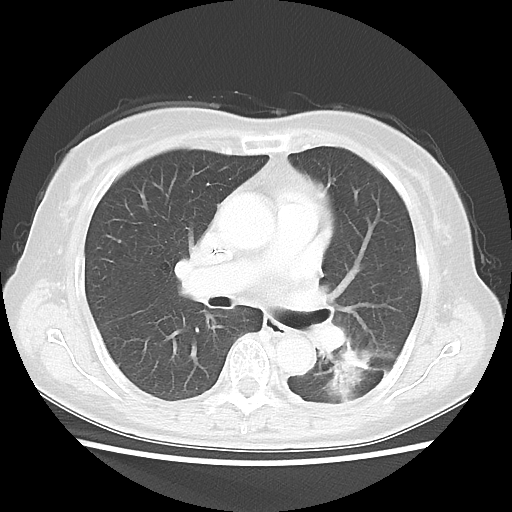
Chest CT, one axial slice. Reconstruction kernel LUNG. Lung window (W 1500 / L -600 HU). 512 × 512 image matrix, field of view 341 × 341 mm. Patient: female, 69 years. Case-level facts recorded for this patient, not image findings: clinical TNM (as recorded): T1c N0 M0.
Structures marked on this image (bounding box drawn by a radiologist):
- lung tumour (recorded histology: adenocarcinoma): bounding box [x1, y1, x2, y2] px = [325, 343, 375, 404]